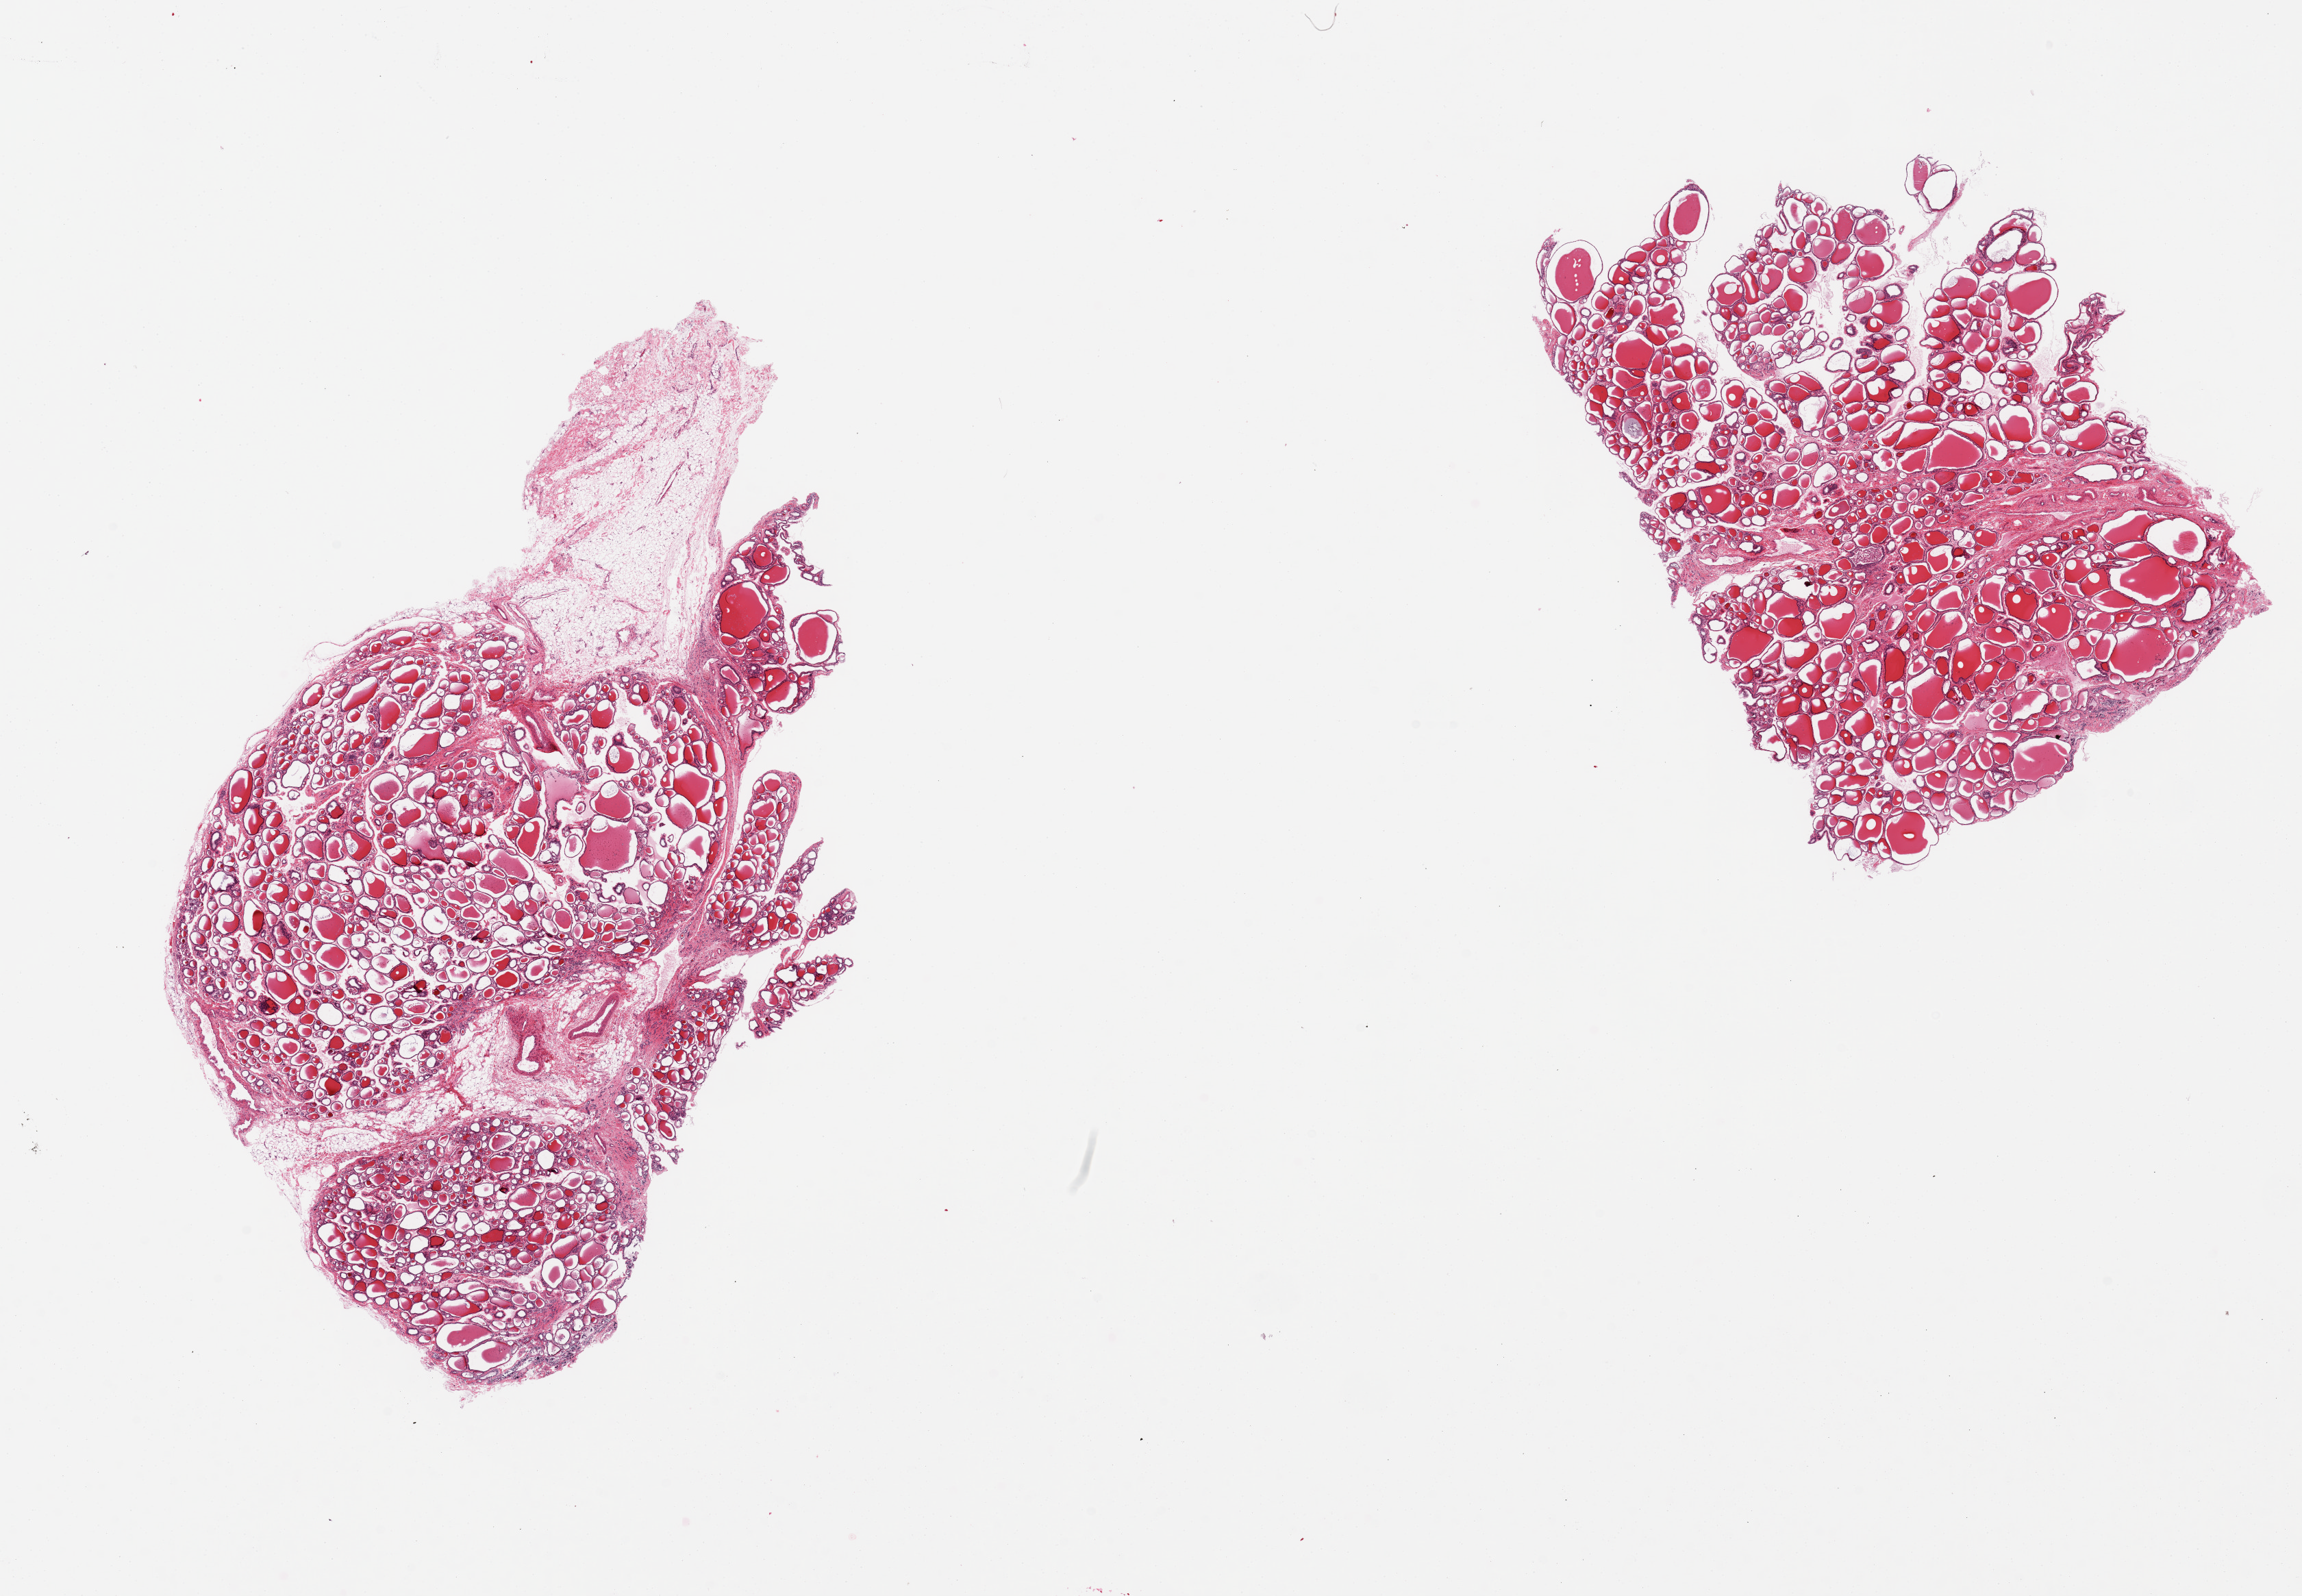
Digitized hematoxylin and eosin (H&E)-stained section — a low-resolution overview of the entire scanned area, about 26.6 x 18.4 mm (from a 20x scan), PAXgene-fixed paraffin-embedded (PFPE) section, target tissue: thyroid, donor tissue sample.
Pathologist's review note for this sample: 2 pieces, one piece includes ~20% fat, multinodular with some cystic change.